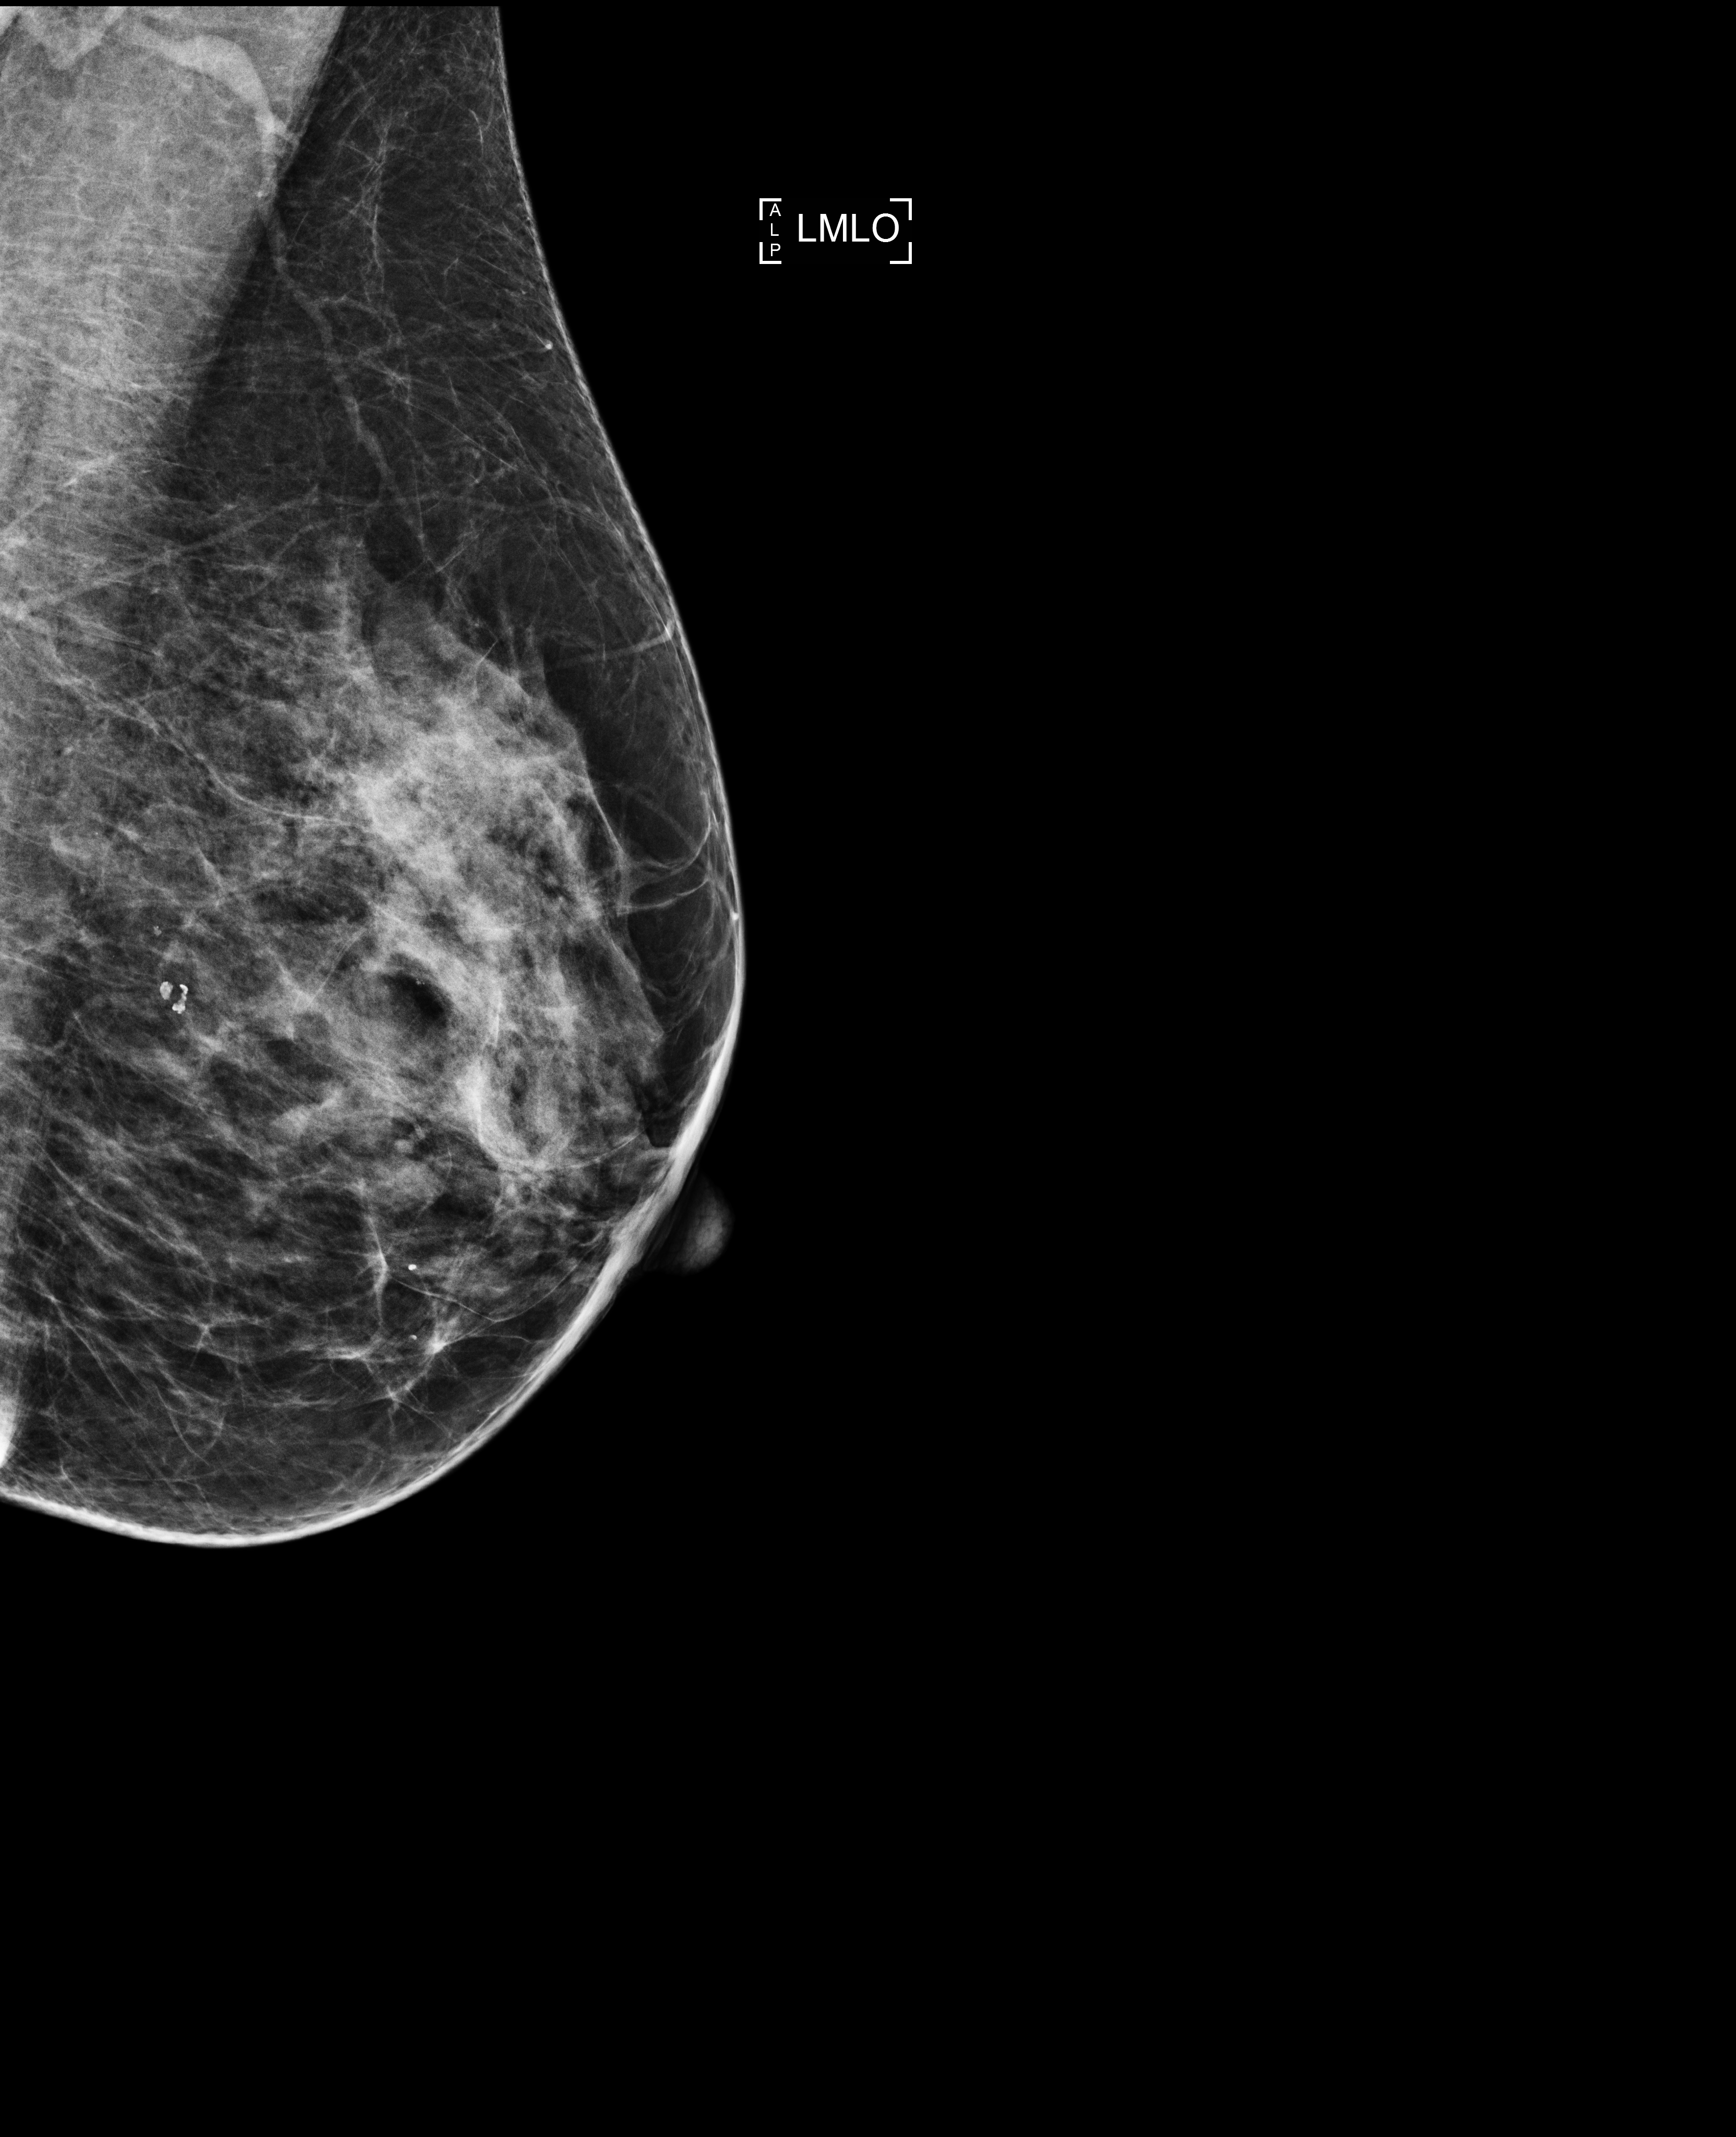
Digital mammogram (FFDM); left breast; MLO view; screening examination; system: Selenia Dimensions. Patient: female, 57 years.
BI-RADS breast density category at the screening exam (both breasts, scale 1–4): 3. Final BI-RADS assessment for this screening round (tomosynthesis exam, both breasts): category 1. Recall: no recall after this screen.